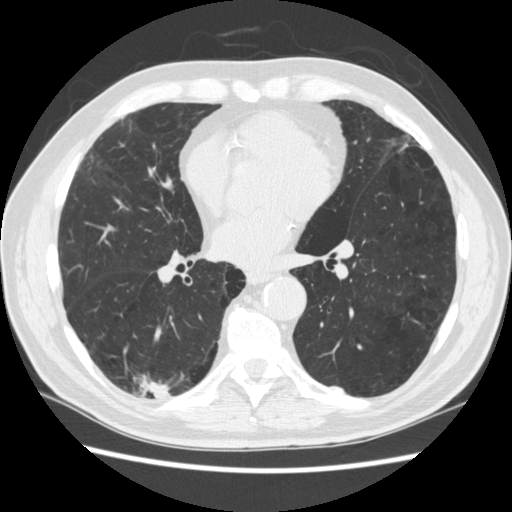
Low-dose screening chest CT, one axial slice. Position 123 of 266 along the scan axis. Reconstruction kernel STANDARD. 120 kVp. Lung window (W 1500 / L -600 HU). 1.25 mm slice thickness. 512 × 512 image matrix, field of view 360 × 360 mm.
Structures marked on this image (manually delineated by an expert):
- lesion 1 (tumor, upper lobe of right lung): box from (x=148, y=382) to (x=169, y=399) px